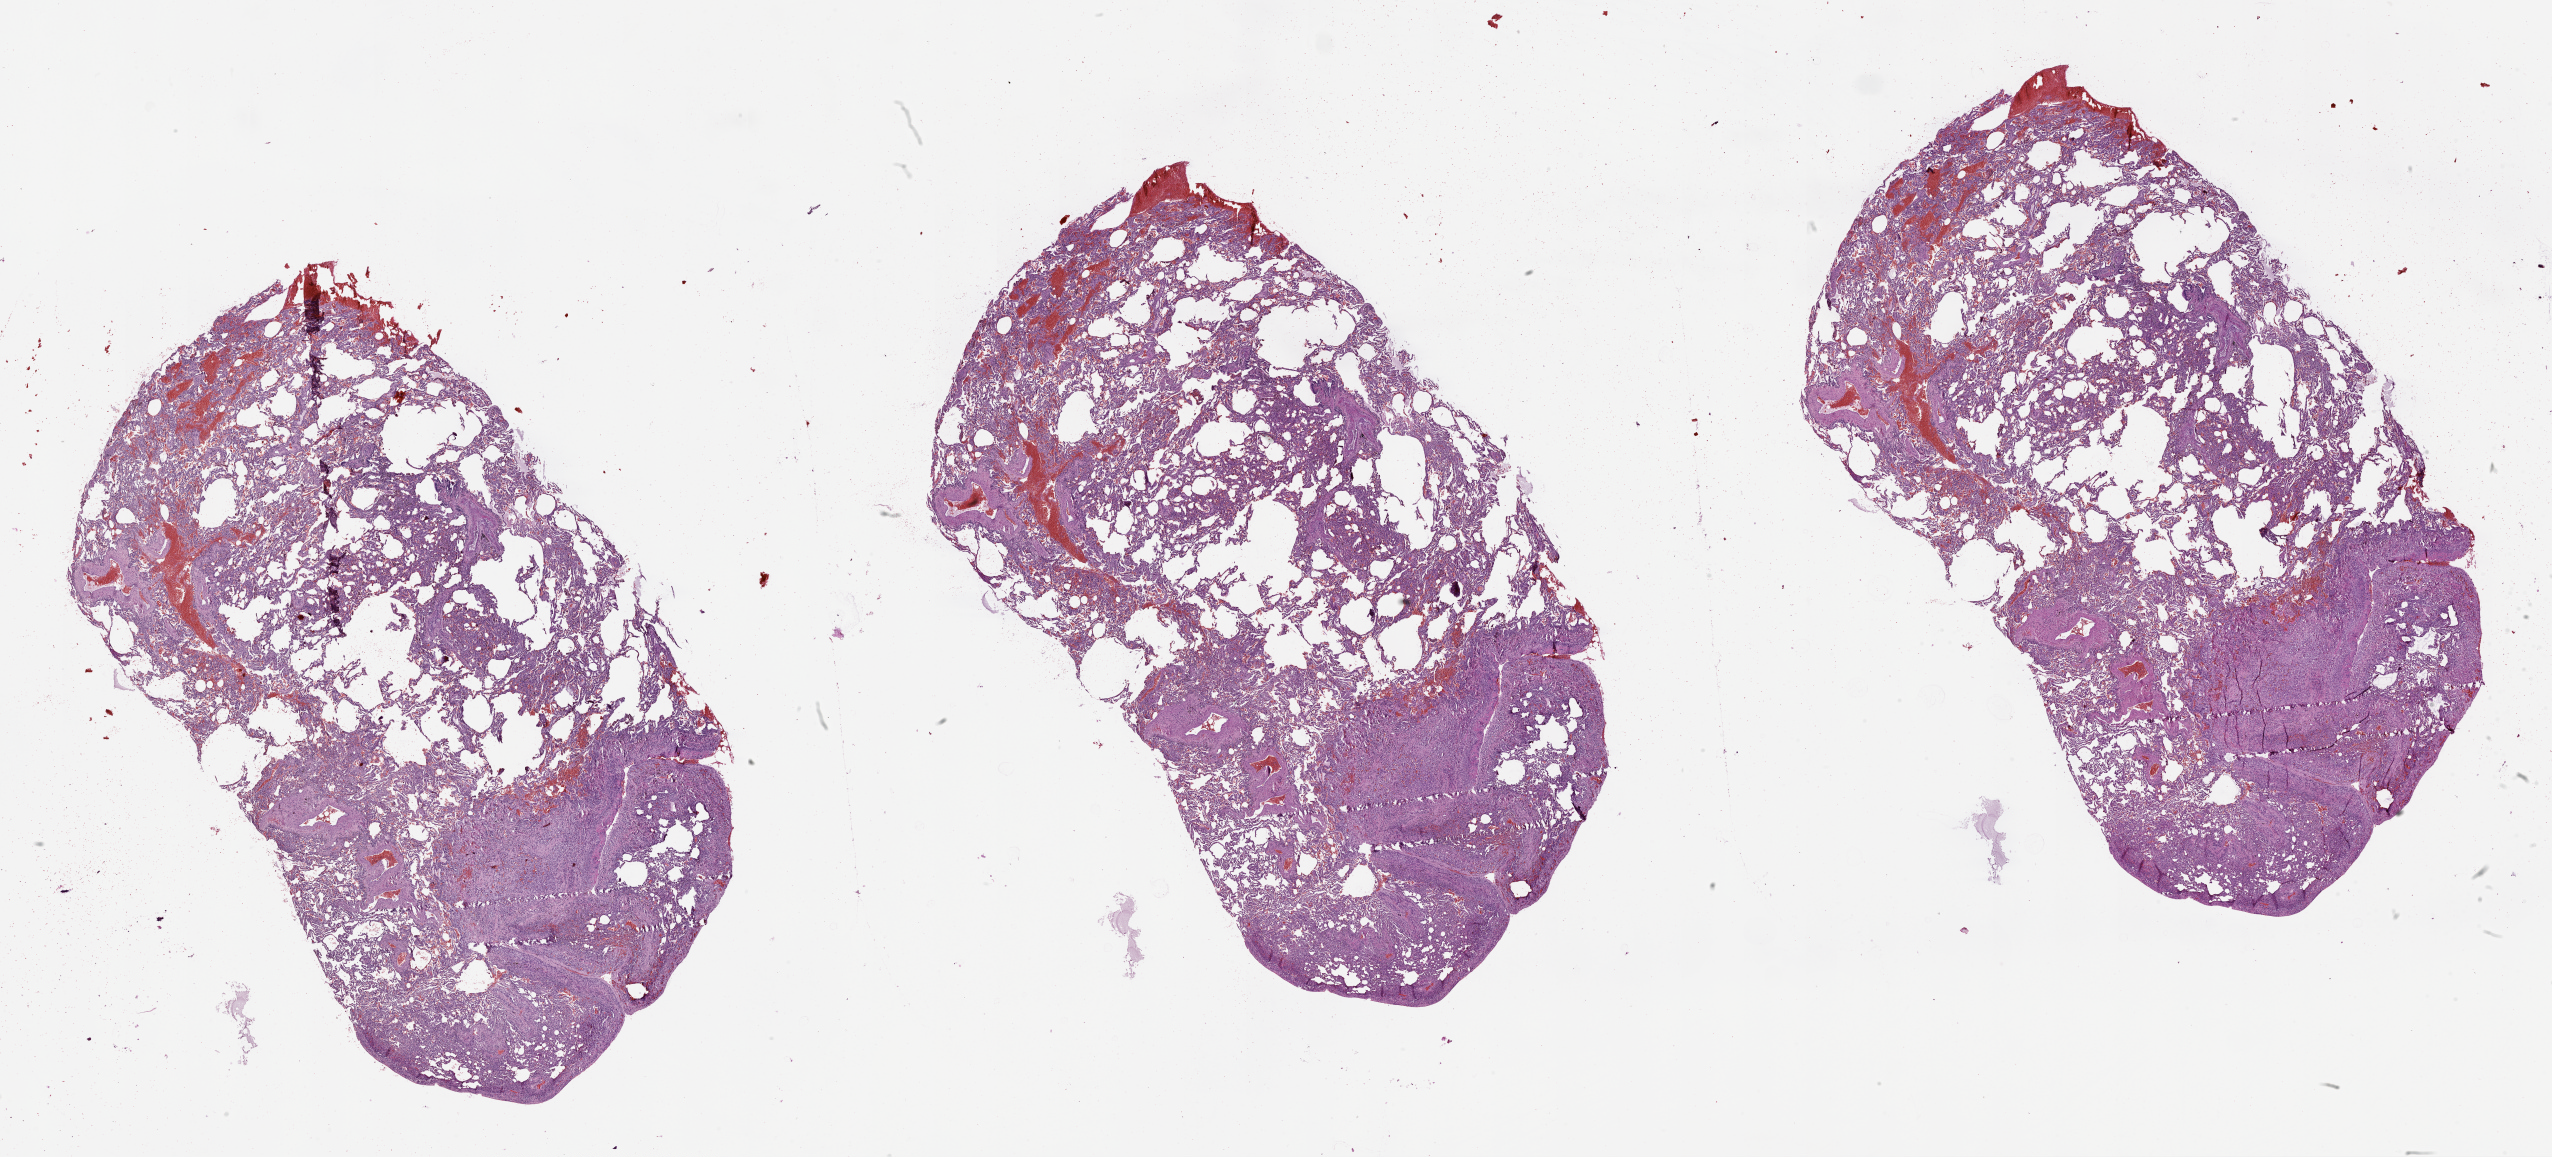
Digitized H&E-stained tissue section (whole slide) — whole scanned area (about 41.1 x 18.6 mm, from a 20x scan) shown as a low-resolution overview. Lung, normal (non-tumour) tissue. Male, 49 y/o.
• this section: normal (non-tumour) tissue from the same patient
• patient diagnosis (cohort enrolment): squamous cell carcinoma (lung)